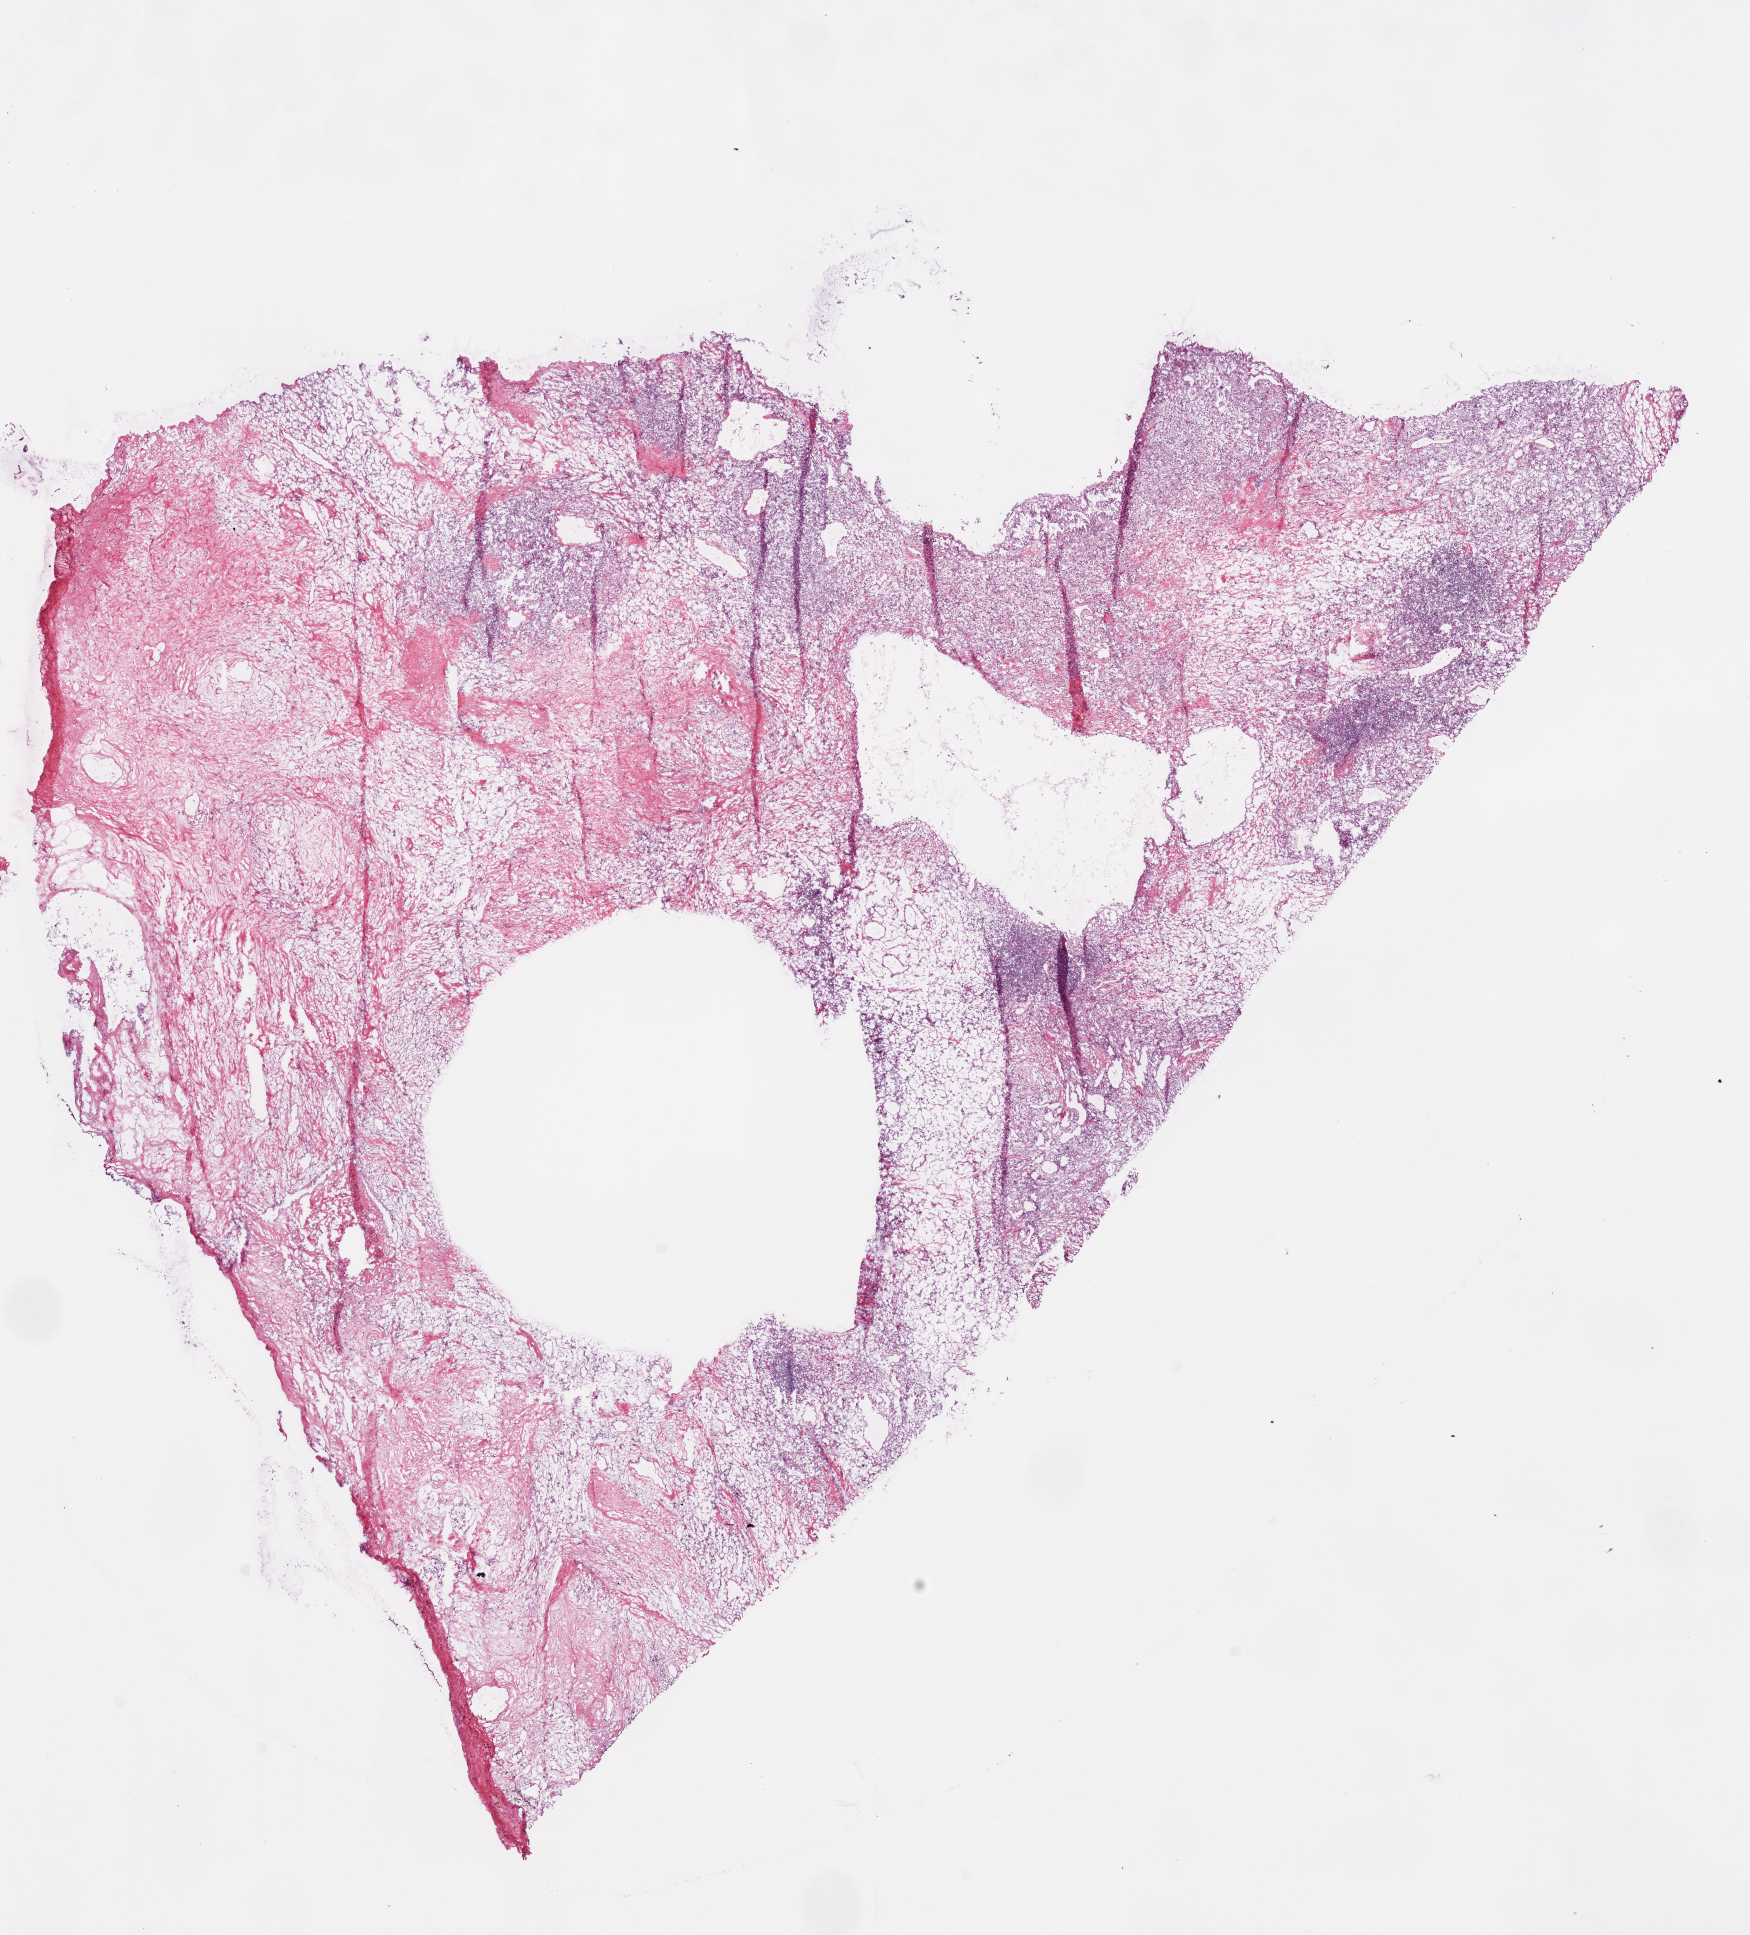
Whole-slide histology image, H&E-stained, low-resolution overview of the scanned area, about 14.0 x 15.5 mm (from a 20x scan); frozen section from the bottom of the tissue portion; kidney, primary tumour sample. Patient: male, age at initial diagnosis 63 years. Histologic grade: G3 (poorly differentiated). Composition of this section per pathologist review: tumour cells 50%, tumour nuclei 60%, normal cells 0%, stromal cells 50%, necrosis 0%.
AJCC pathologic stage: IV. Pathologic diagnosis: Clear cell adenocarcinoma, NOS. TNM: T3a N0 M1.